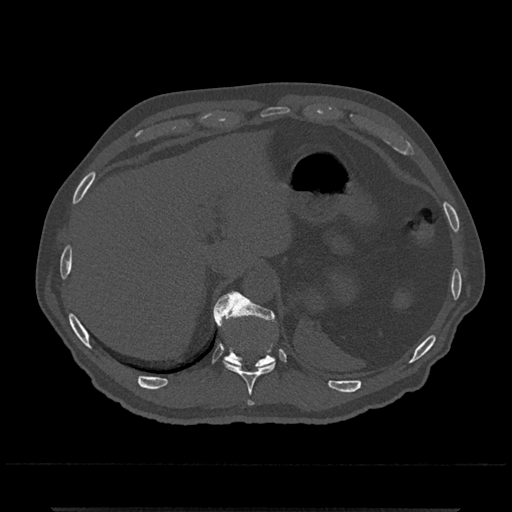
CT including the spine, one axial slice. Slice 529 of 797 in the series (ordered by position). Bone window (W 1800 / L 400 HU). 512 × 512 image matrix, field of view 393 × 393 mm. Male patient, age 67 years. From the clinical record (not read from this slice): primary cancer: prostate.
Annotated regions visible in this slice (semi-automatic segmentation, software-assisted and operator-edited):
- T10 vertebra: bounding box (x1, y1, x2, y2) in pixels: (218, 292, 276, 406)
- T11 vertebra: (213, 292, 277, 368)